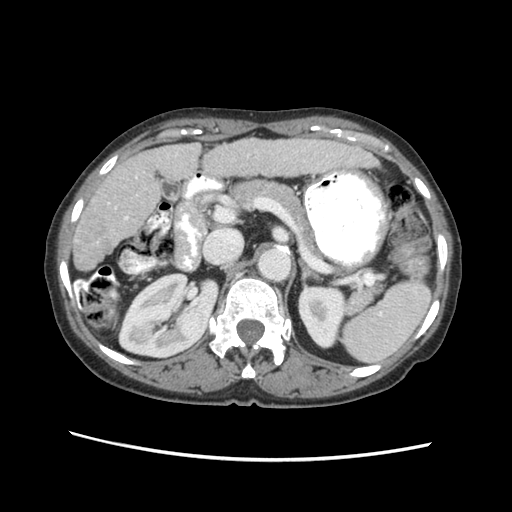
Contrast-enhanced abdominal CT (liver protocol), one axial slice. Slice 27 of 63 in the series (ordered by position). Reconstruction kernel STANDARD. 120 kVp. Soft-tissue window (W 400 / L 40 HU). 2.5 mm slice thickness. 512 × 512 image matrix. From the clinical record (not read from this slice): diagnosis: hepatocellular carcinoma (patient treated with transarterial chemoembolisation; whether this scan precedes or follows treatment is not stated here); TNM stage (as recorded): Stage-I; Child-Pugh class: B; tumour differentiation: well differentiated; tumour nodularity: uninodular.
Outlined on this slice (semi-automatic segmentation, software-assisted and operator-edited):
- liver parenchyma outside the tumour (the mass and vessels are separate outlines, so this box may not span the whole liver): box from (x=70, y=134) to (x=388, y=270) px
- liver vessels: (x=122, y=150)–(x=301, y=218)